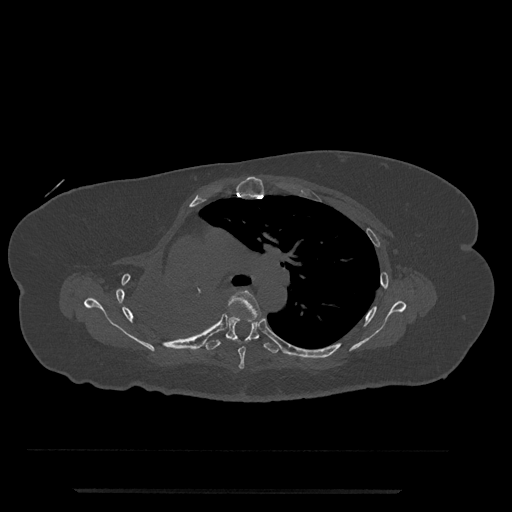
CT including the spine, one axial slice. Slice 517 of 797 in the series (ordered by position). Reconstruction kernel Br40s/3. 120 kVp. Bone window (W 1800 / L 400 HU). 512 × 512 image matrix, field of view 440 × 440 mm. Female patient, age 51 years. From the clinical record (not read from this slice): primary cancer: neuro; vertebrae with lytic lesions (as recorded): T8.
Annotated regions visible in this slice (semi-automatic segmentation, software-assisted and operator-edited):
- T5 vertebra: bounding box [x1, y1, x2, y2] px = [197, 290, 263, 369]
- T6 vertebra: [206, 317, 279, 354]